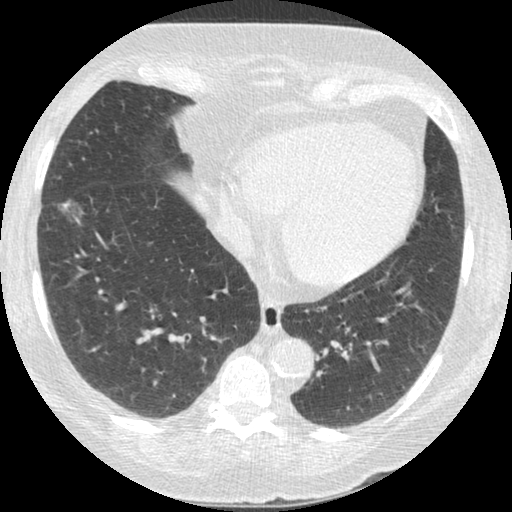
Low-dose screening chest CT, one axial slice; position 94 of 245 along the scan axis; reconstruction kernel STANDARD; 120 kVp; lung window (W 1500 / L -600 HU); 1.25 mm slice thickness; 512 × 512 image matrix, field of view 310 × 310 mm.
Structures marked on this image (manually delineated by an expert):
- lesion 1 (tumor, lower lobe of right lung): bounding box <59,199,83,222> (left, top, right, bottom; pixels)